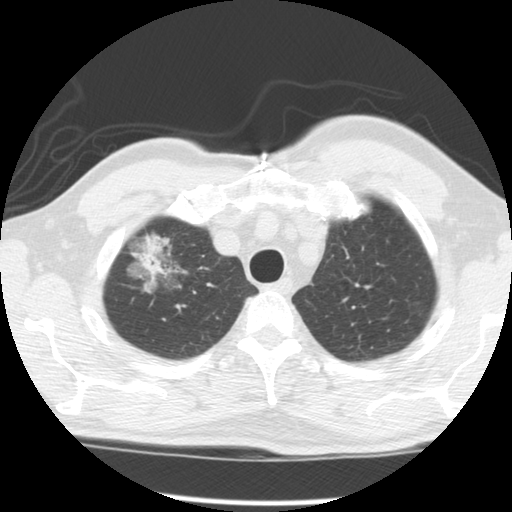
Low-dose screening chest CT, axial slice, second annual screen, lung window (W 1500 / L -600 HU), 2.5 mm slice thickness, standard (soft-tissue) reconstruction kernel (STANDARD), slice 19 of 120 in the series. Male, age 64 years at enrolment. Former smoker at enrolment.
- Expert-annotated lung lesion, bounding box [x1, y1, x2, y2] px = [121, 231, 194, 302].
- The screening reader recorded 2 non-calcified nodules or masses ≥4 mm on this exam; which of them this box marks is not recorded.
- Official screen result: positive, other.
- Later outcome: lung cancer diagnosed 429 days after this screen (after the third annual screen) — adenocarcinoma, NOS, right upper lobe, well differentiated (G1), stage IB (AJCC 6th edition), 45 mm at pathology.